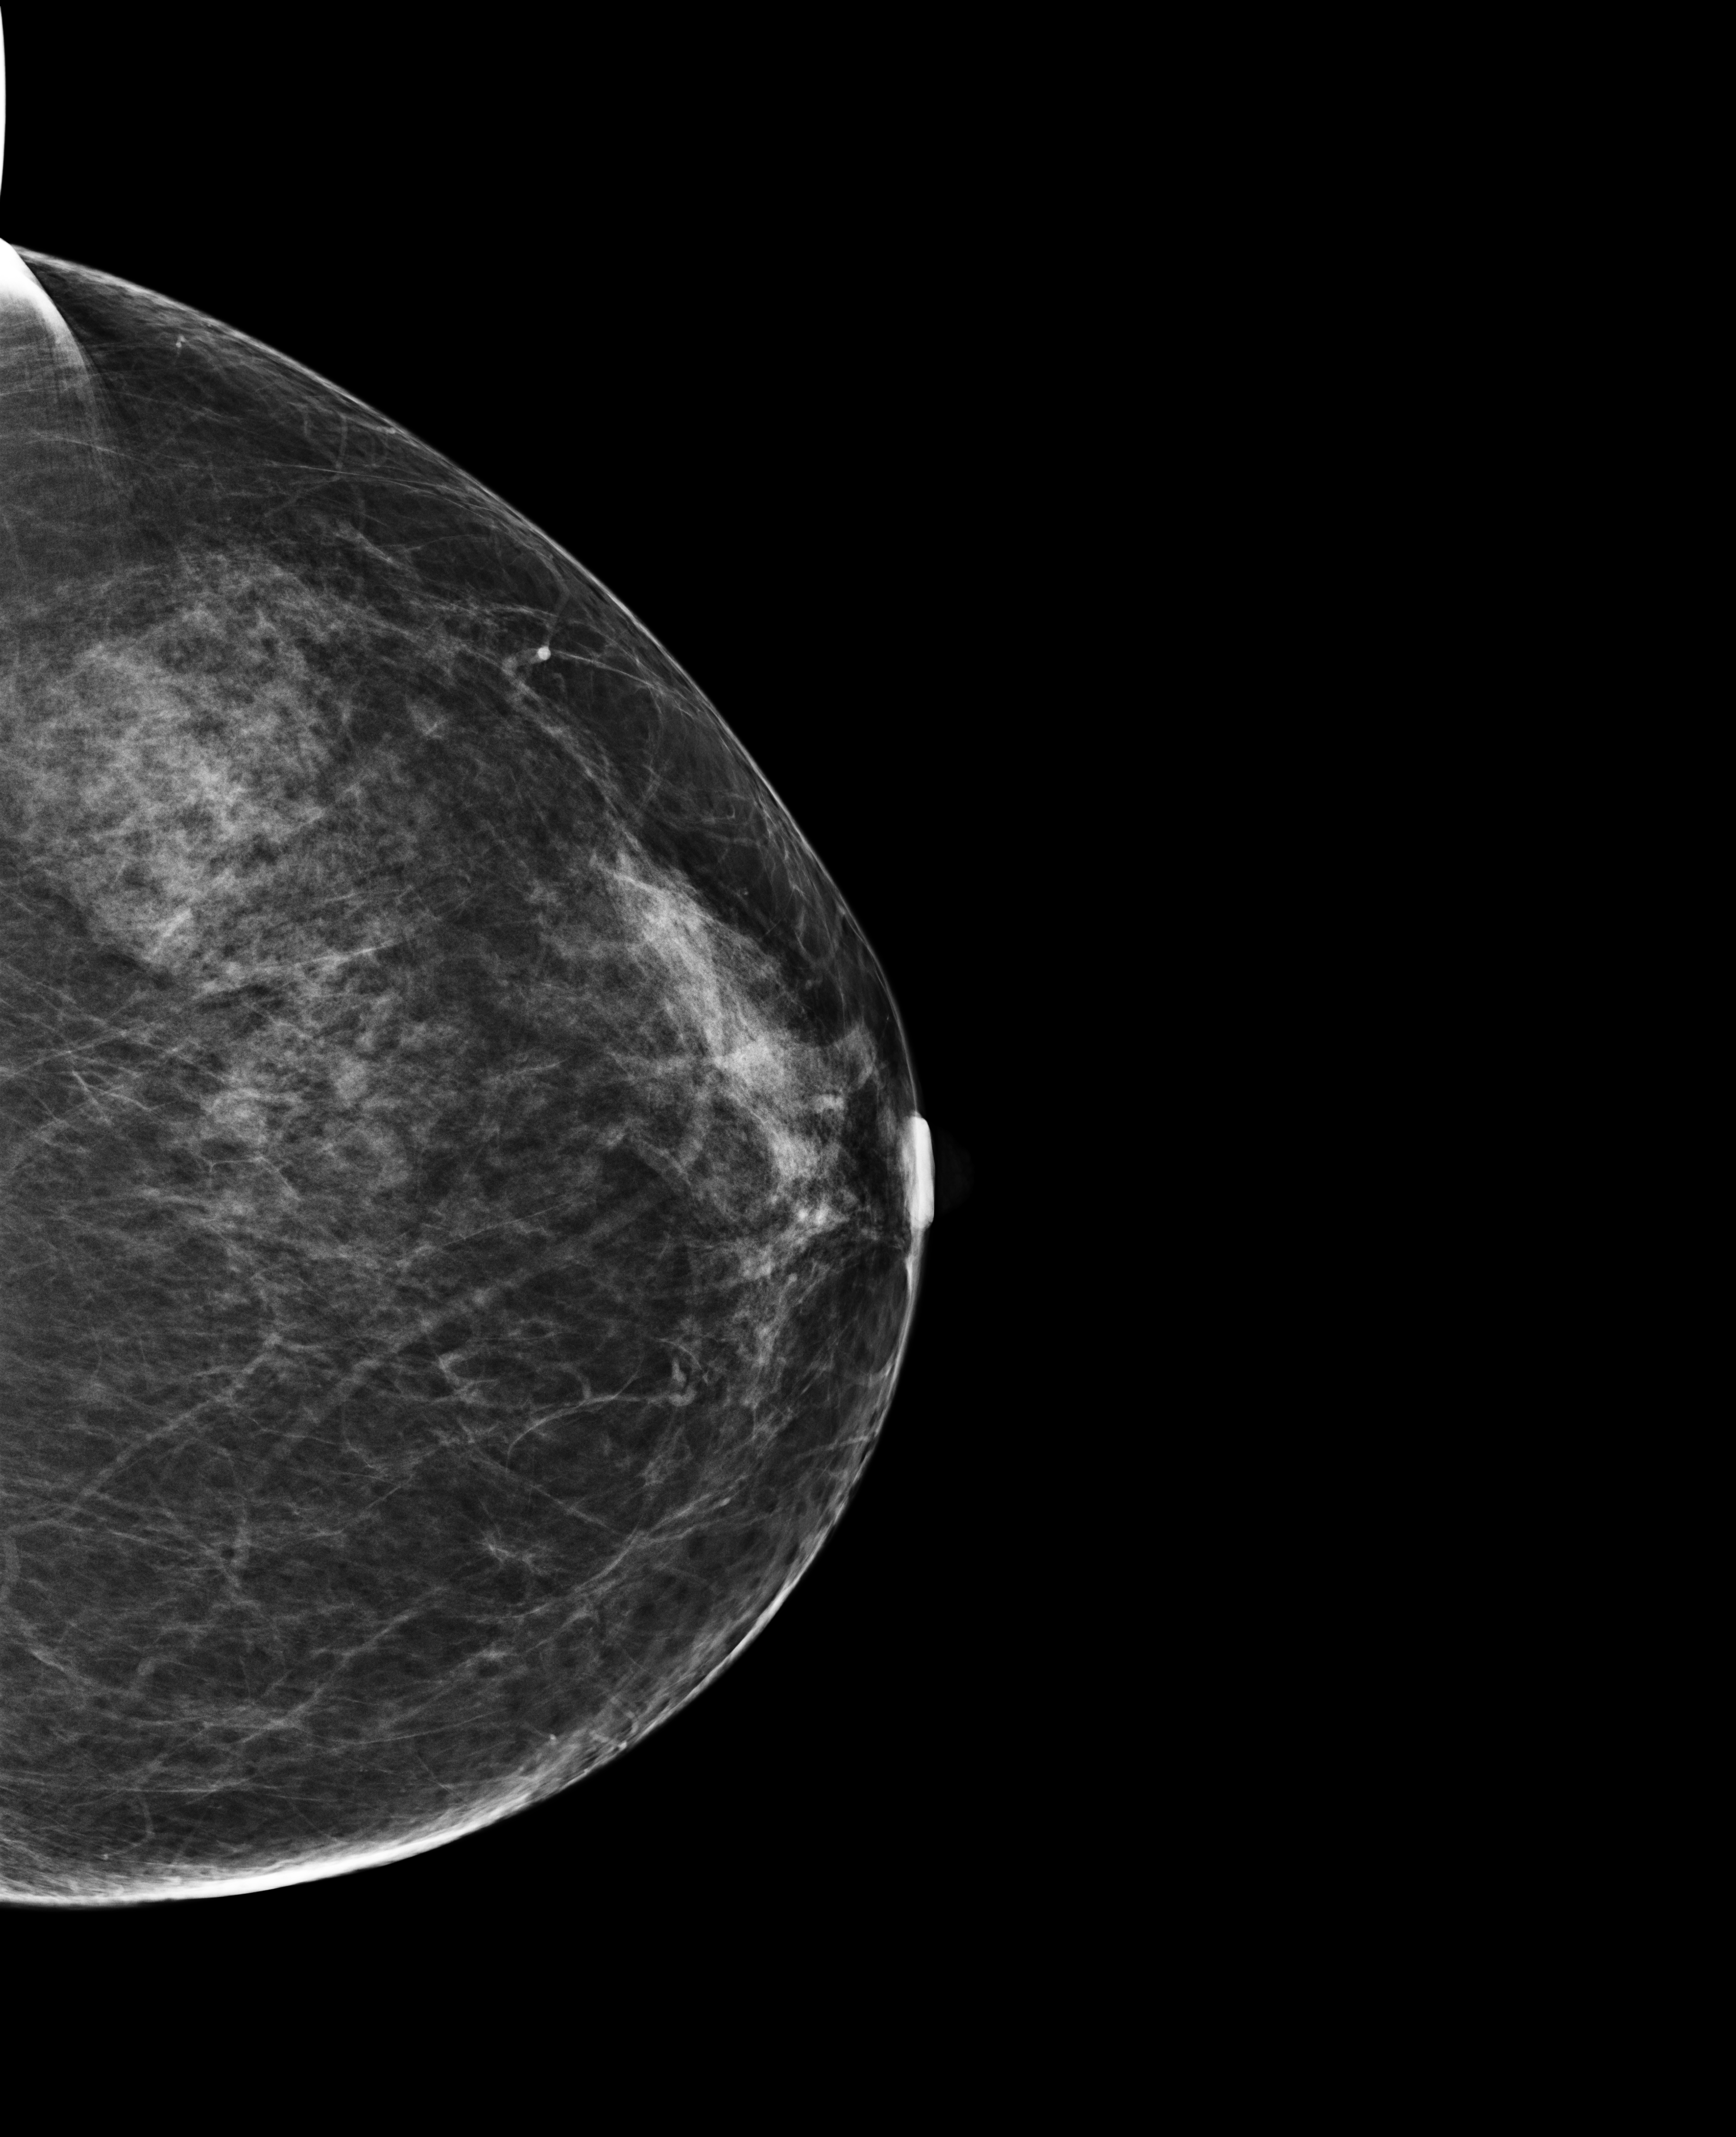
Annual screening mammography examination, system: Selenia Dimensions. Patient: female, 47 years.
Image type: full-field digital mammogram. Breast: left. Projection: cranio-caudal projection.